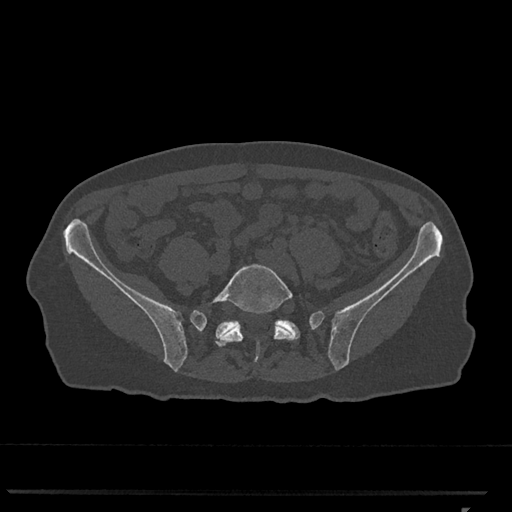
CT including the spine, one axial slice. 120 kVp. Bone window (W 1800 / L 400 HU). 0.5 mm slice thickness. 512 × 512 image matrix, field of view 380 × 380 mm. Female patient, age 62 years. Case-level facts recorded for this patient, not image findings: primary cancer: renal.
Outlined on this slice (semi-automatically segmented with operator editing):
- L5 vertebra: box from (x=207, y=264) to (x=297, y=362) px